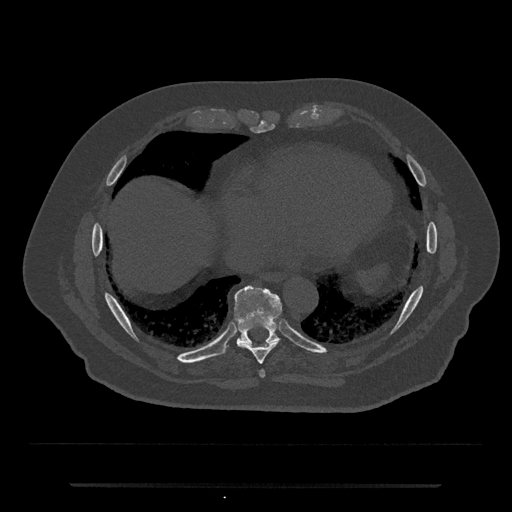
CT including the spine, one axial slice. Position 783 of 797 along the scan axis. Reconstruction kernel Br40s/3. Bone window (W 1800 / L 400 HU). 0.5 mm slice thickness. 512 × 512 image matrix. Male patient, age 80 years. From the clinical record (not read from this slice): primary cancer: prostate; vertebrae with lytic lesions (as recorded): L1, T11.
Structures marked on this image (semi-automatic segmentation, software-assisted and operator-edited):
- T8 vertebra: box from (x=238, y=326) to (x=279, y=364) px
- T9 vertebra: (x=219, y=286)–(x=282, y=354)